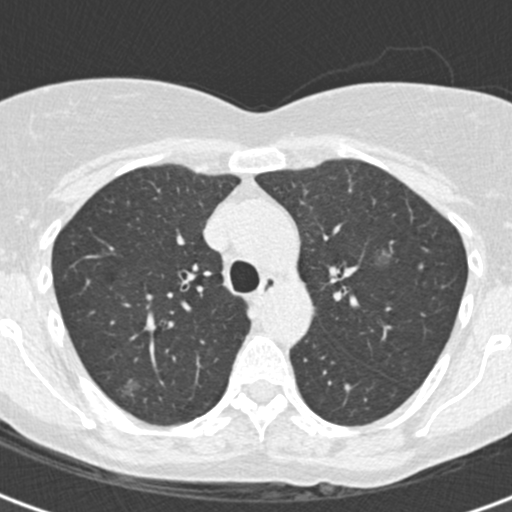
Low-dose screening chest CT, one axial slice; position 124 of 172 along the scan axis; reconstruction kernel B30f; 120 kVp; lung window (W 1500 / L -600 HU); 2 mm slice thickness; 512 × 512 image matrix.
Structures marked on this image (manually delineated by an expert):
- lesion 1 (tumor, upper lobe of right lung): box from (x=121, y=378) to (x=142, y=397) px